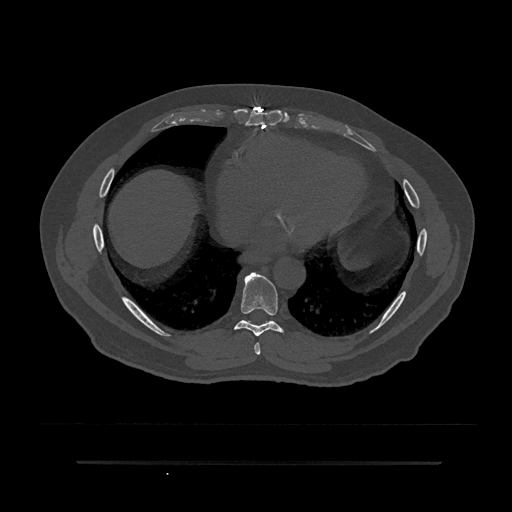
CT including the spine, one axial slice; slice 426 of 797 in the series (ordered by position); bone window (W 1800 / L 400 HU); 512 × 512 image matrix. Patient: male, 59 years. From the clinical record (not read from this slice): primary cancer: bile ducts; vertebrae with lytic lesions (as recorded): T10.
Annotated regions visible in this slice (semi-automatic segmentation, software-assisted and operator-edited):
- T7 vertebra: bounding box [x1, y1, x2, y2] px = [254, 343, 261, 355]
- T8 vertebra: [234, 272, 284, 336]